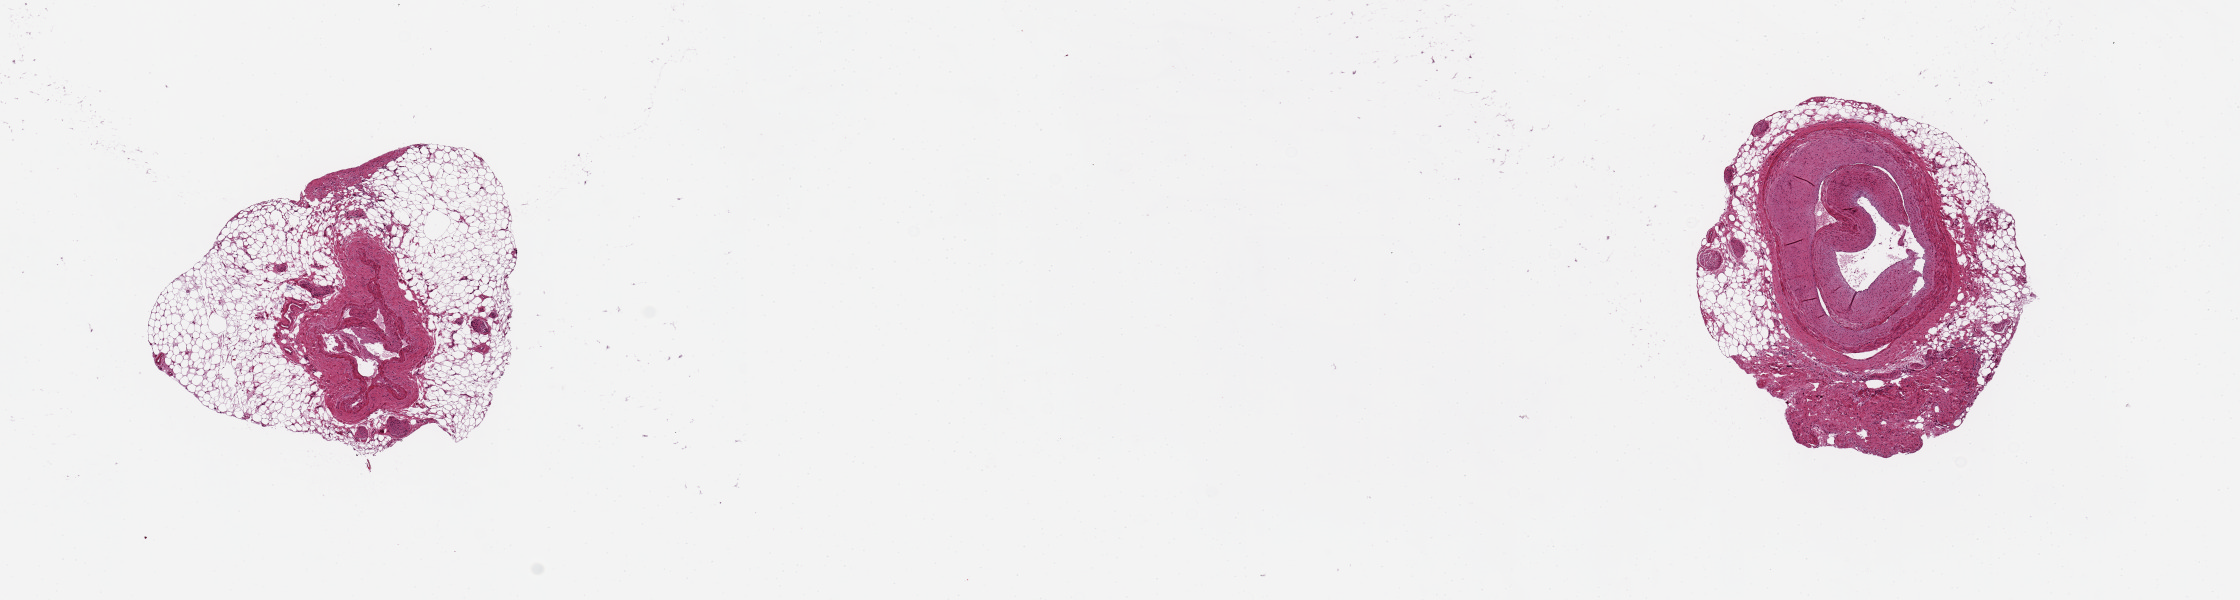
Whole-slide image, H&E stain — whole scanned area (about 17.7 x 4.7 mm) shown as a low-resolution overview. PAXgene-fixed, paraffin-embedded tissue. Sampled site (target tissue): coronary artery. Tissue donor sample. Donor sex: female.
Reviewer comment on this tissue sample: 1 artery, 1 vein; abundant fat around vessels.